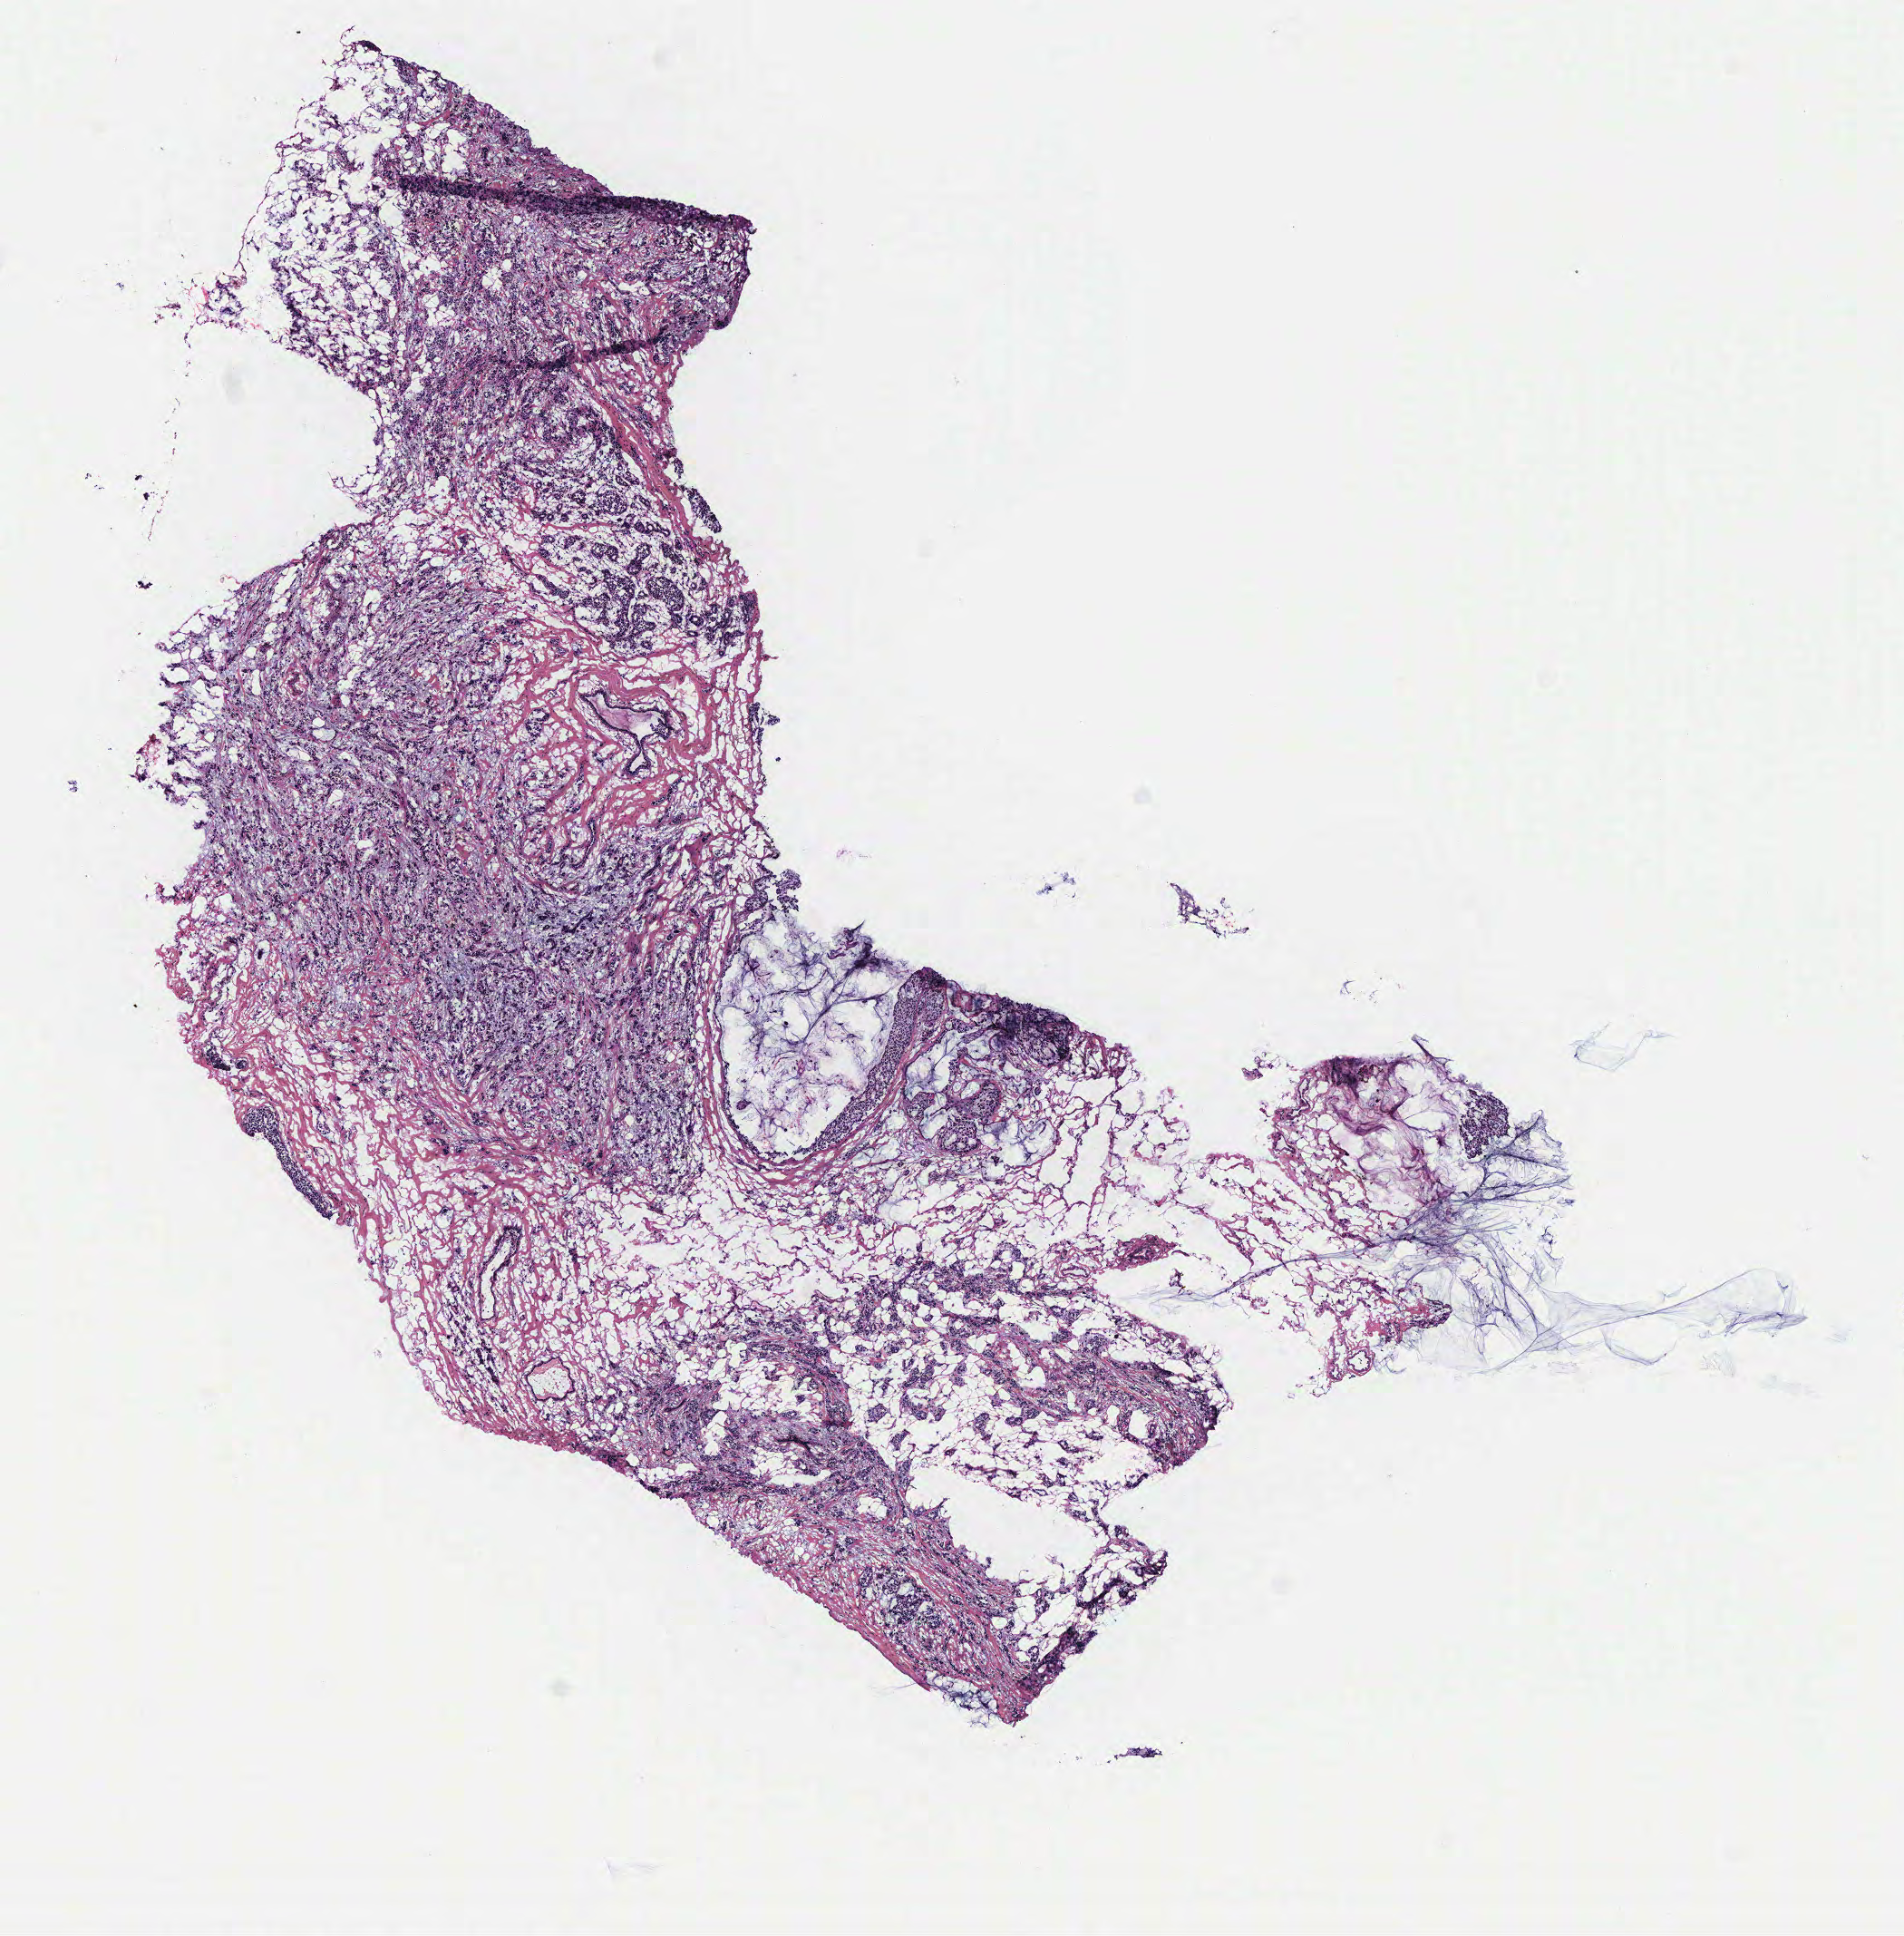
Digitized H&E tissue section (whole slide), shown as a low-resolution overview of the whole scanned area (about 8.4 x 8.5 mm). Breast, tissue type not recorded. 37-year-old female patient.
Patient diagnosis: Infiltrating duct carcinoma, NOS.